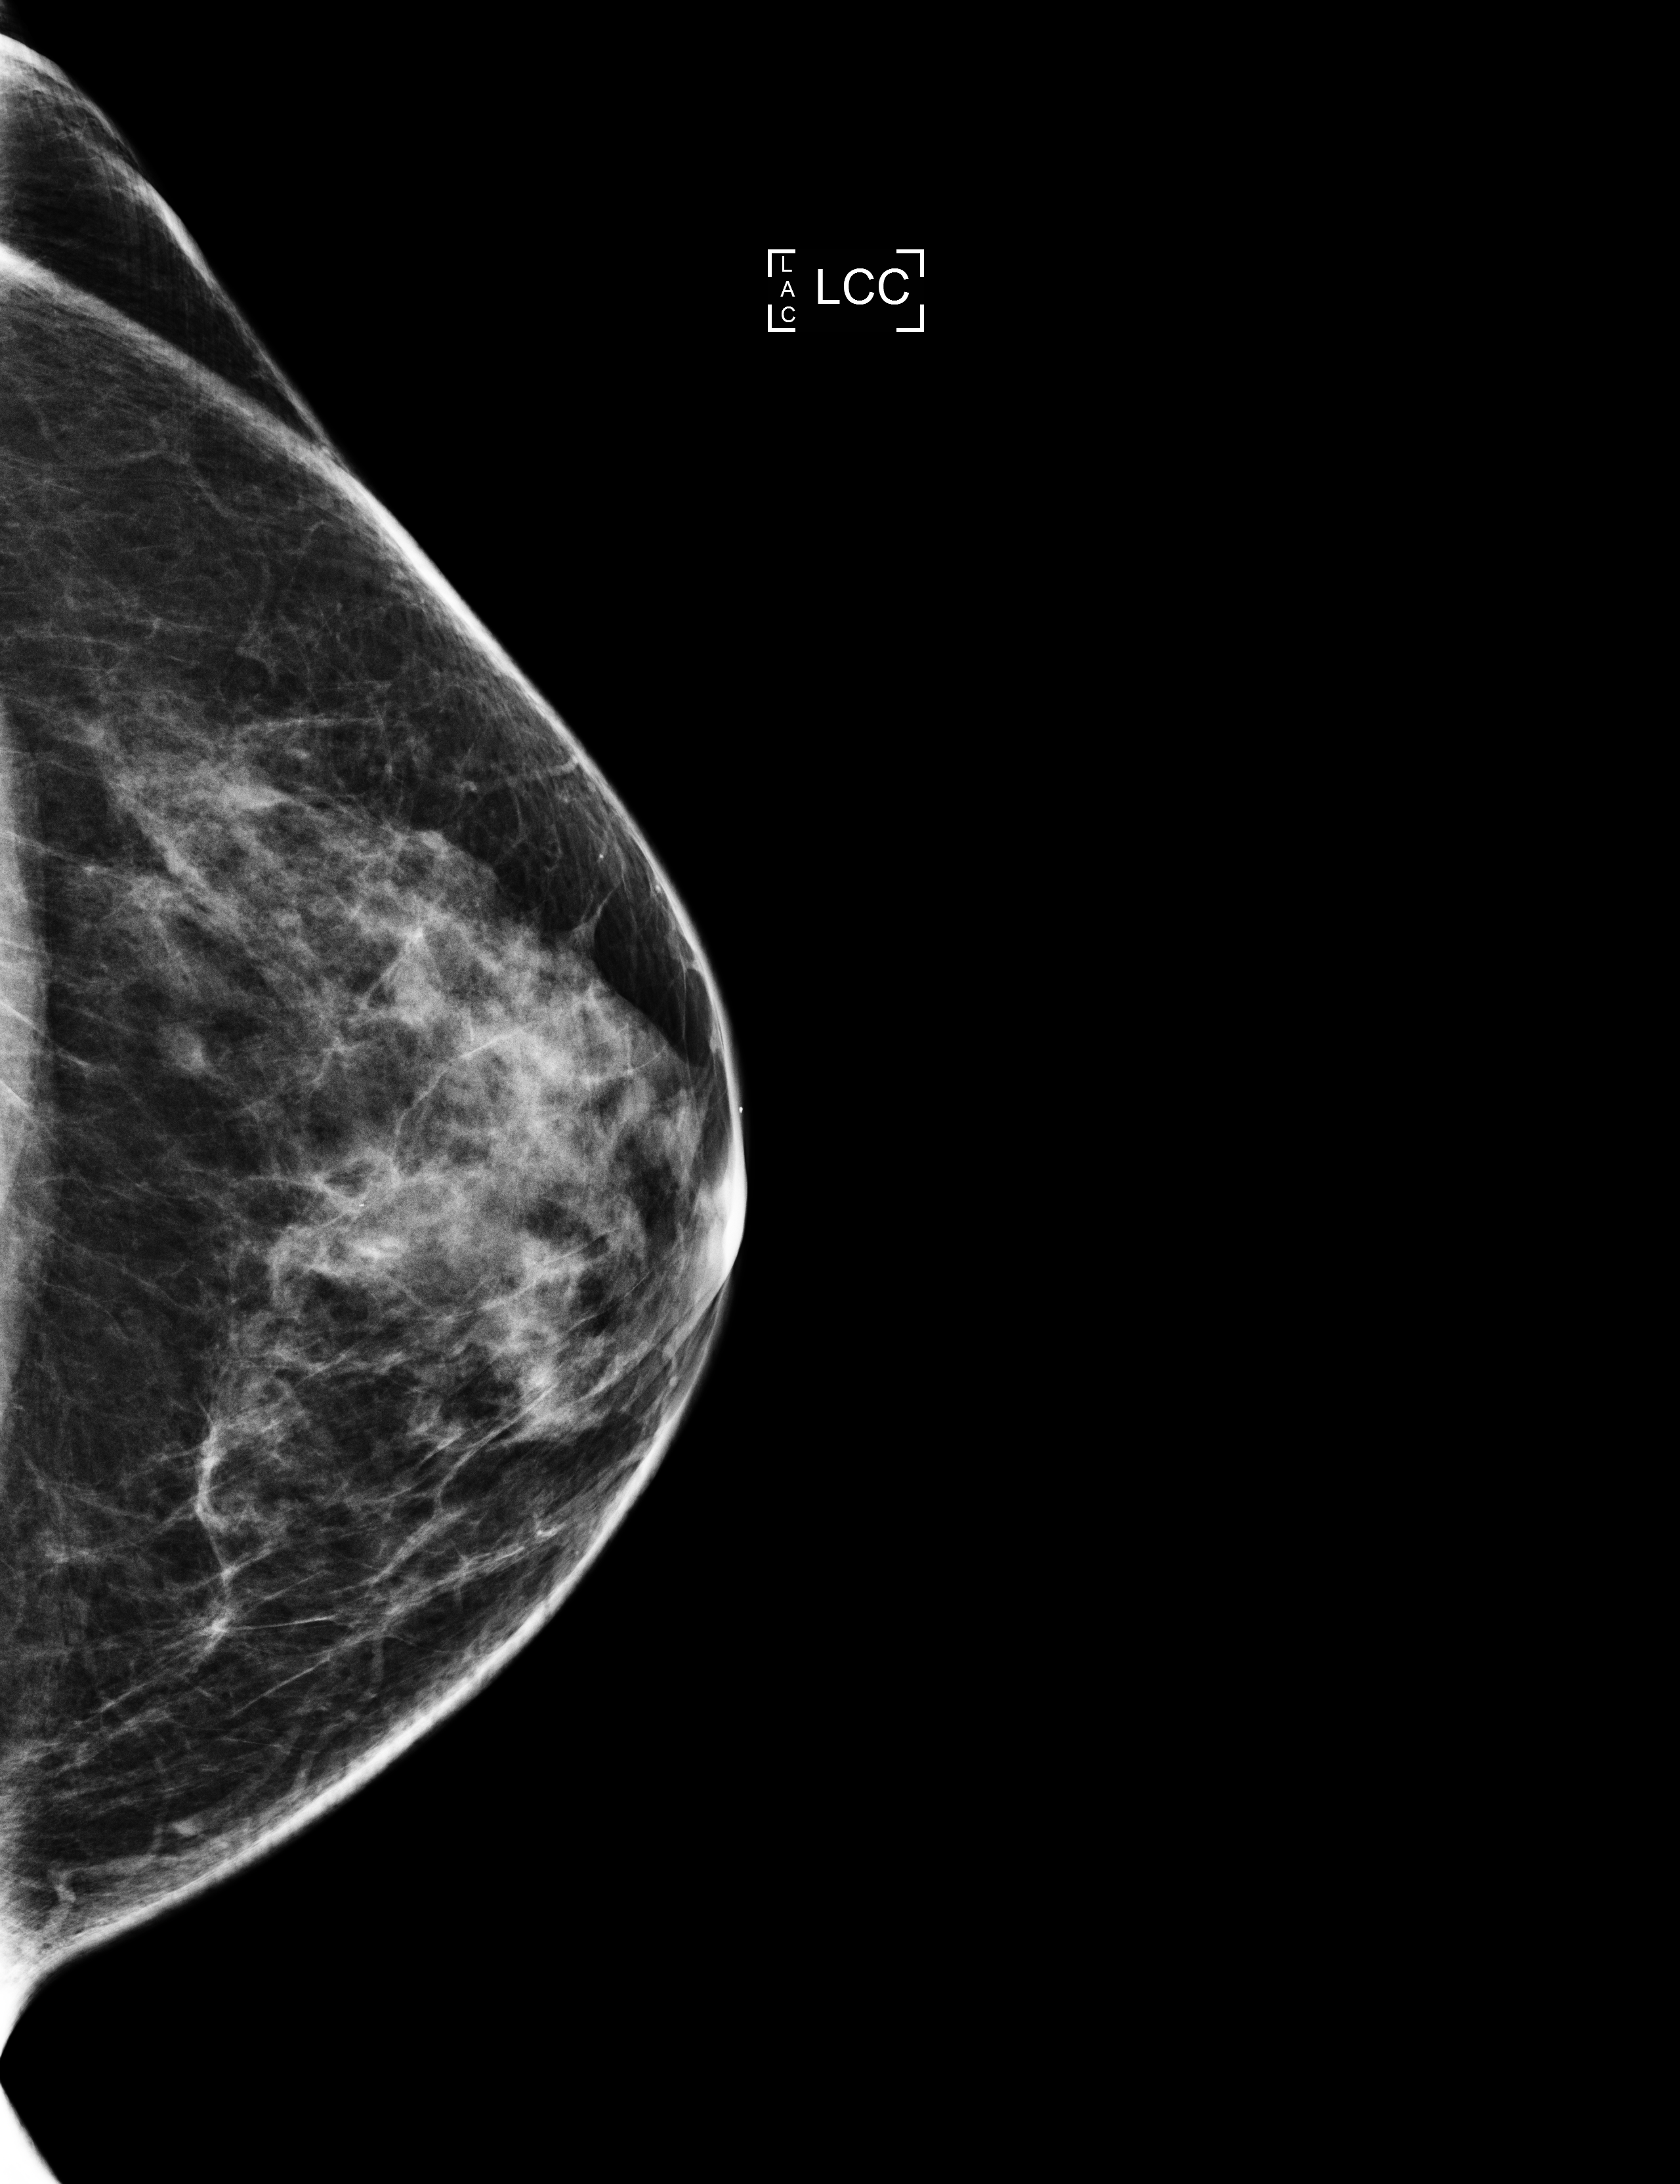
Annual screening mammography examination. Patient: female, 45 years.
Image type: full-field digital mammogram. Breast: left. Projection: cranio-caudal projection.